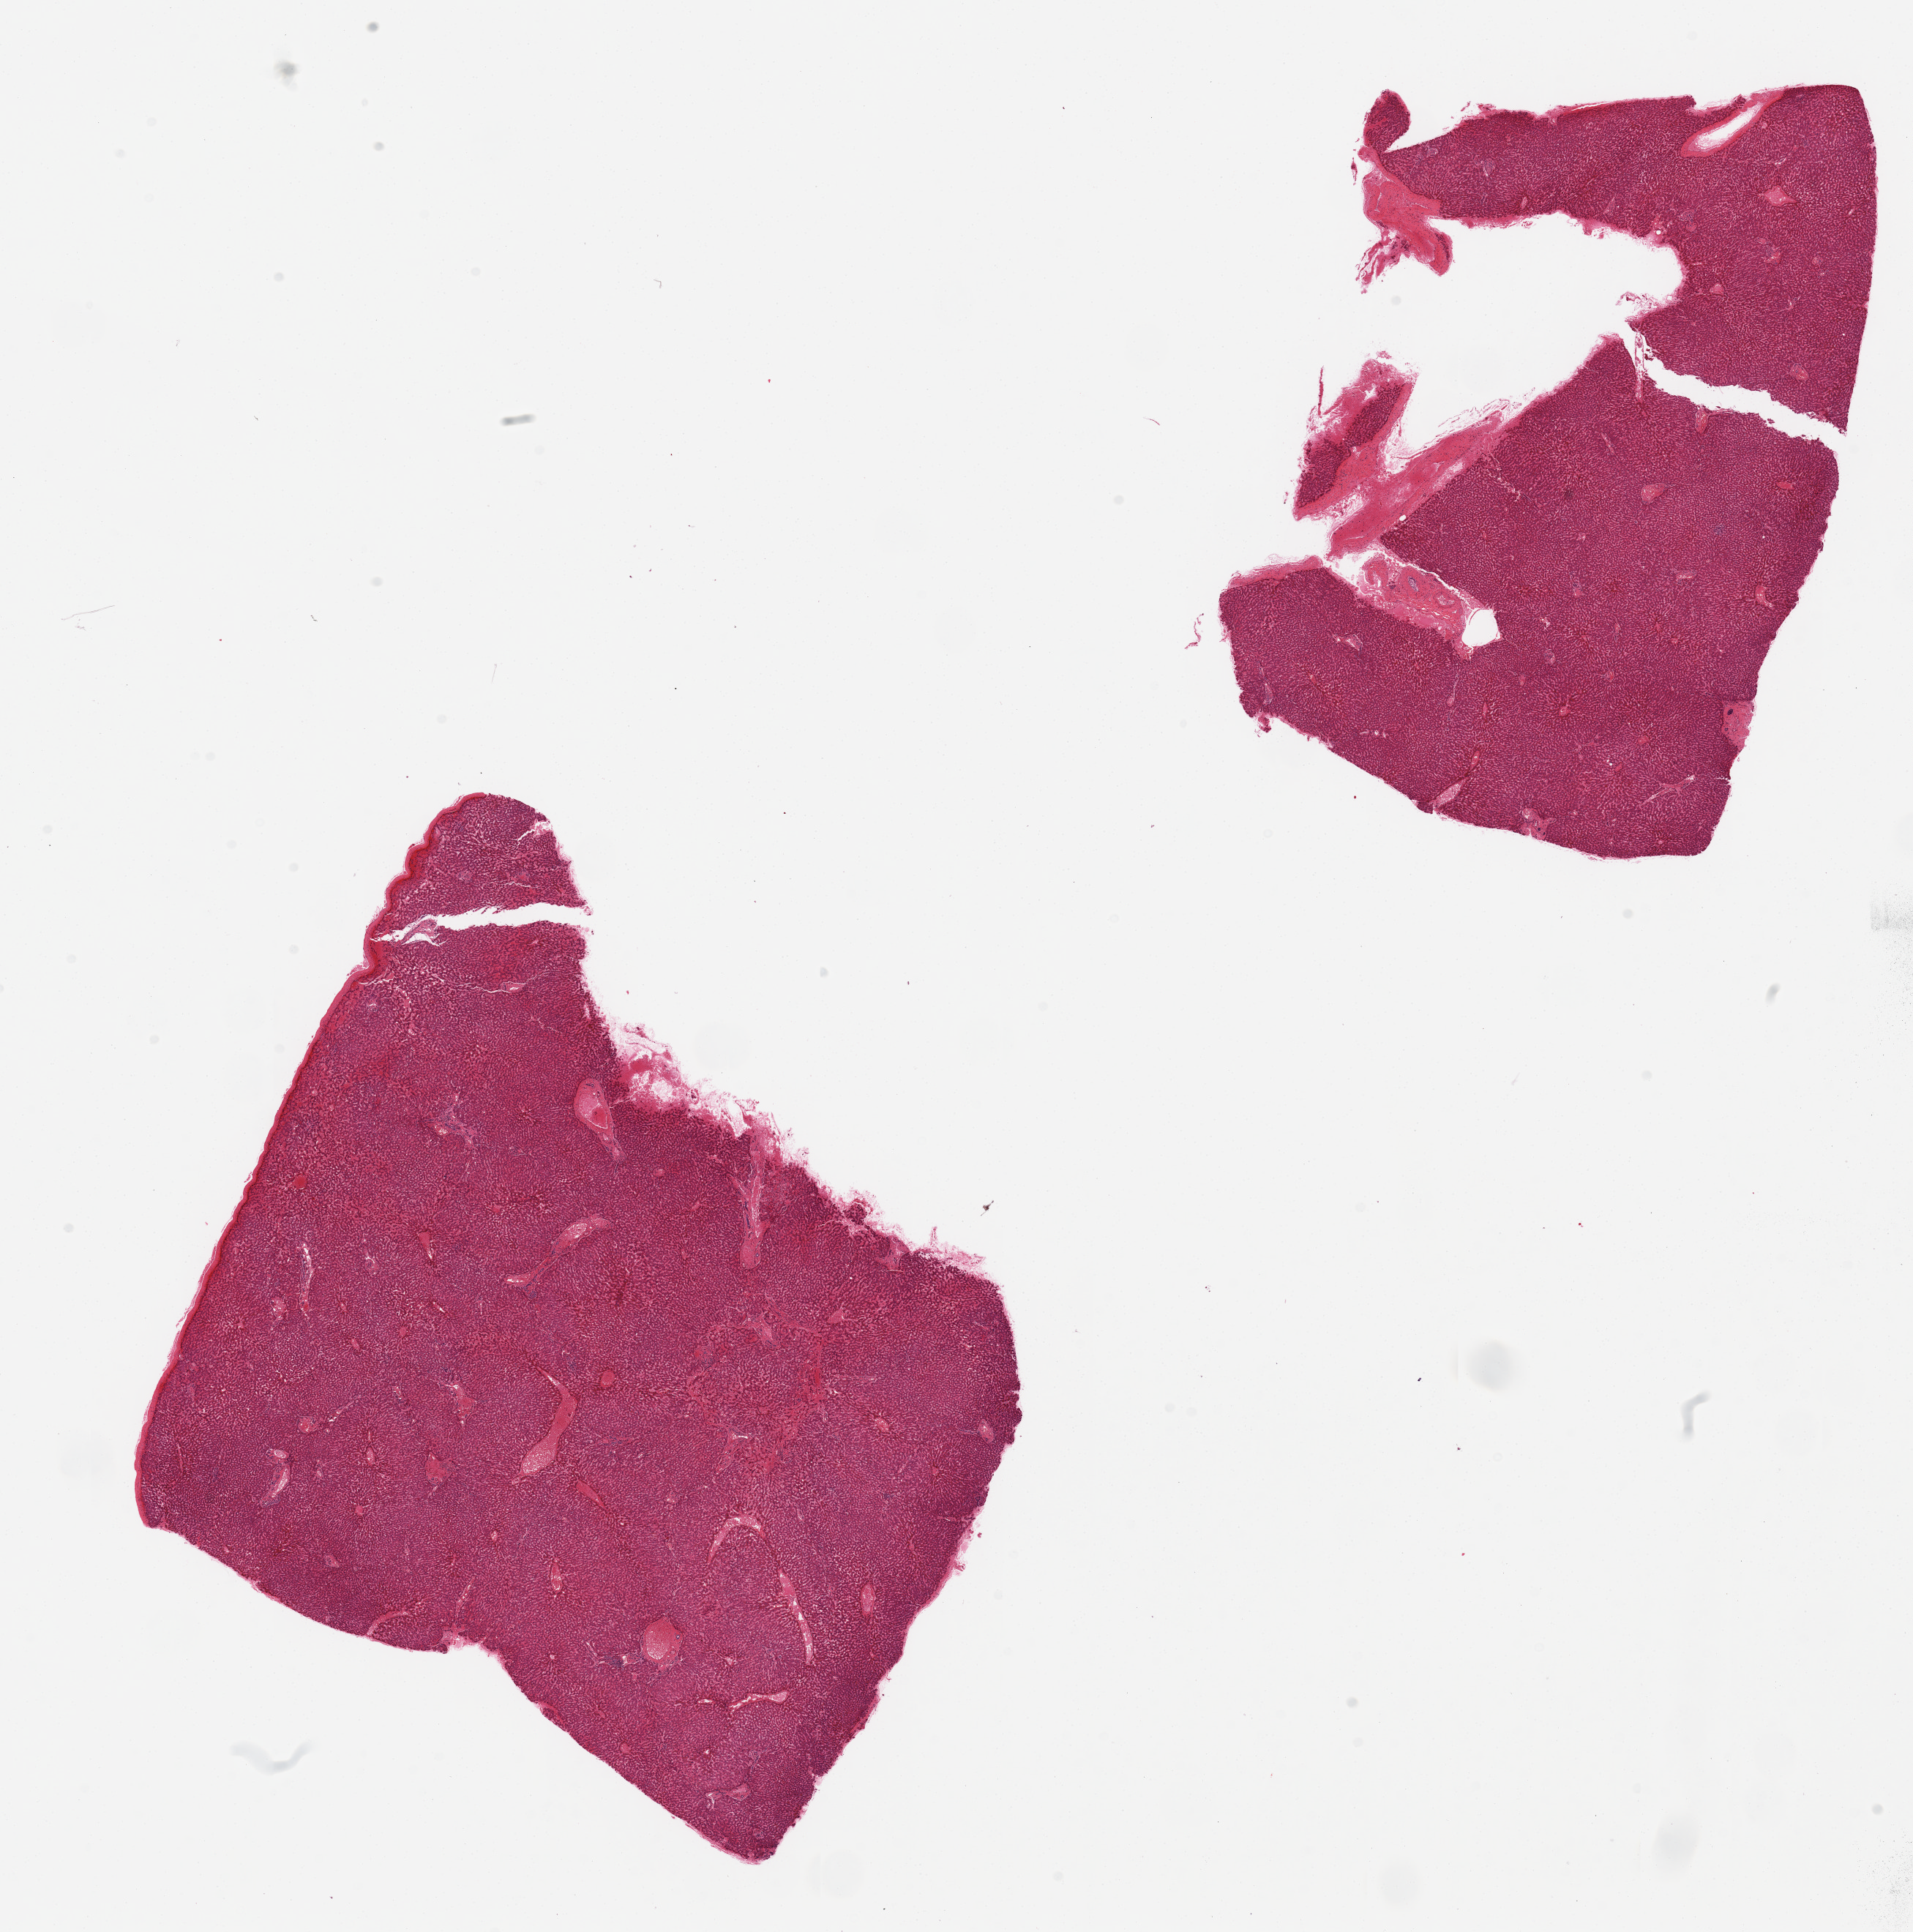
Digitized H&E-stained section — a low-resolution overview of the entire scanned area, about 20.7 x 20.9 mm (acquisition: 20x scan), PAXgene-fixed paraffin-embedded (PFPE) section, sampled site (target tissue): liver, tissue donor sample. Donor: female.
Pathologist's review note for this sample: 2 pieces; capsule present on one piece.